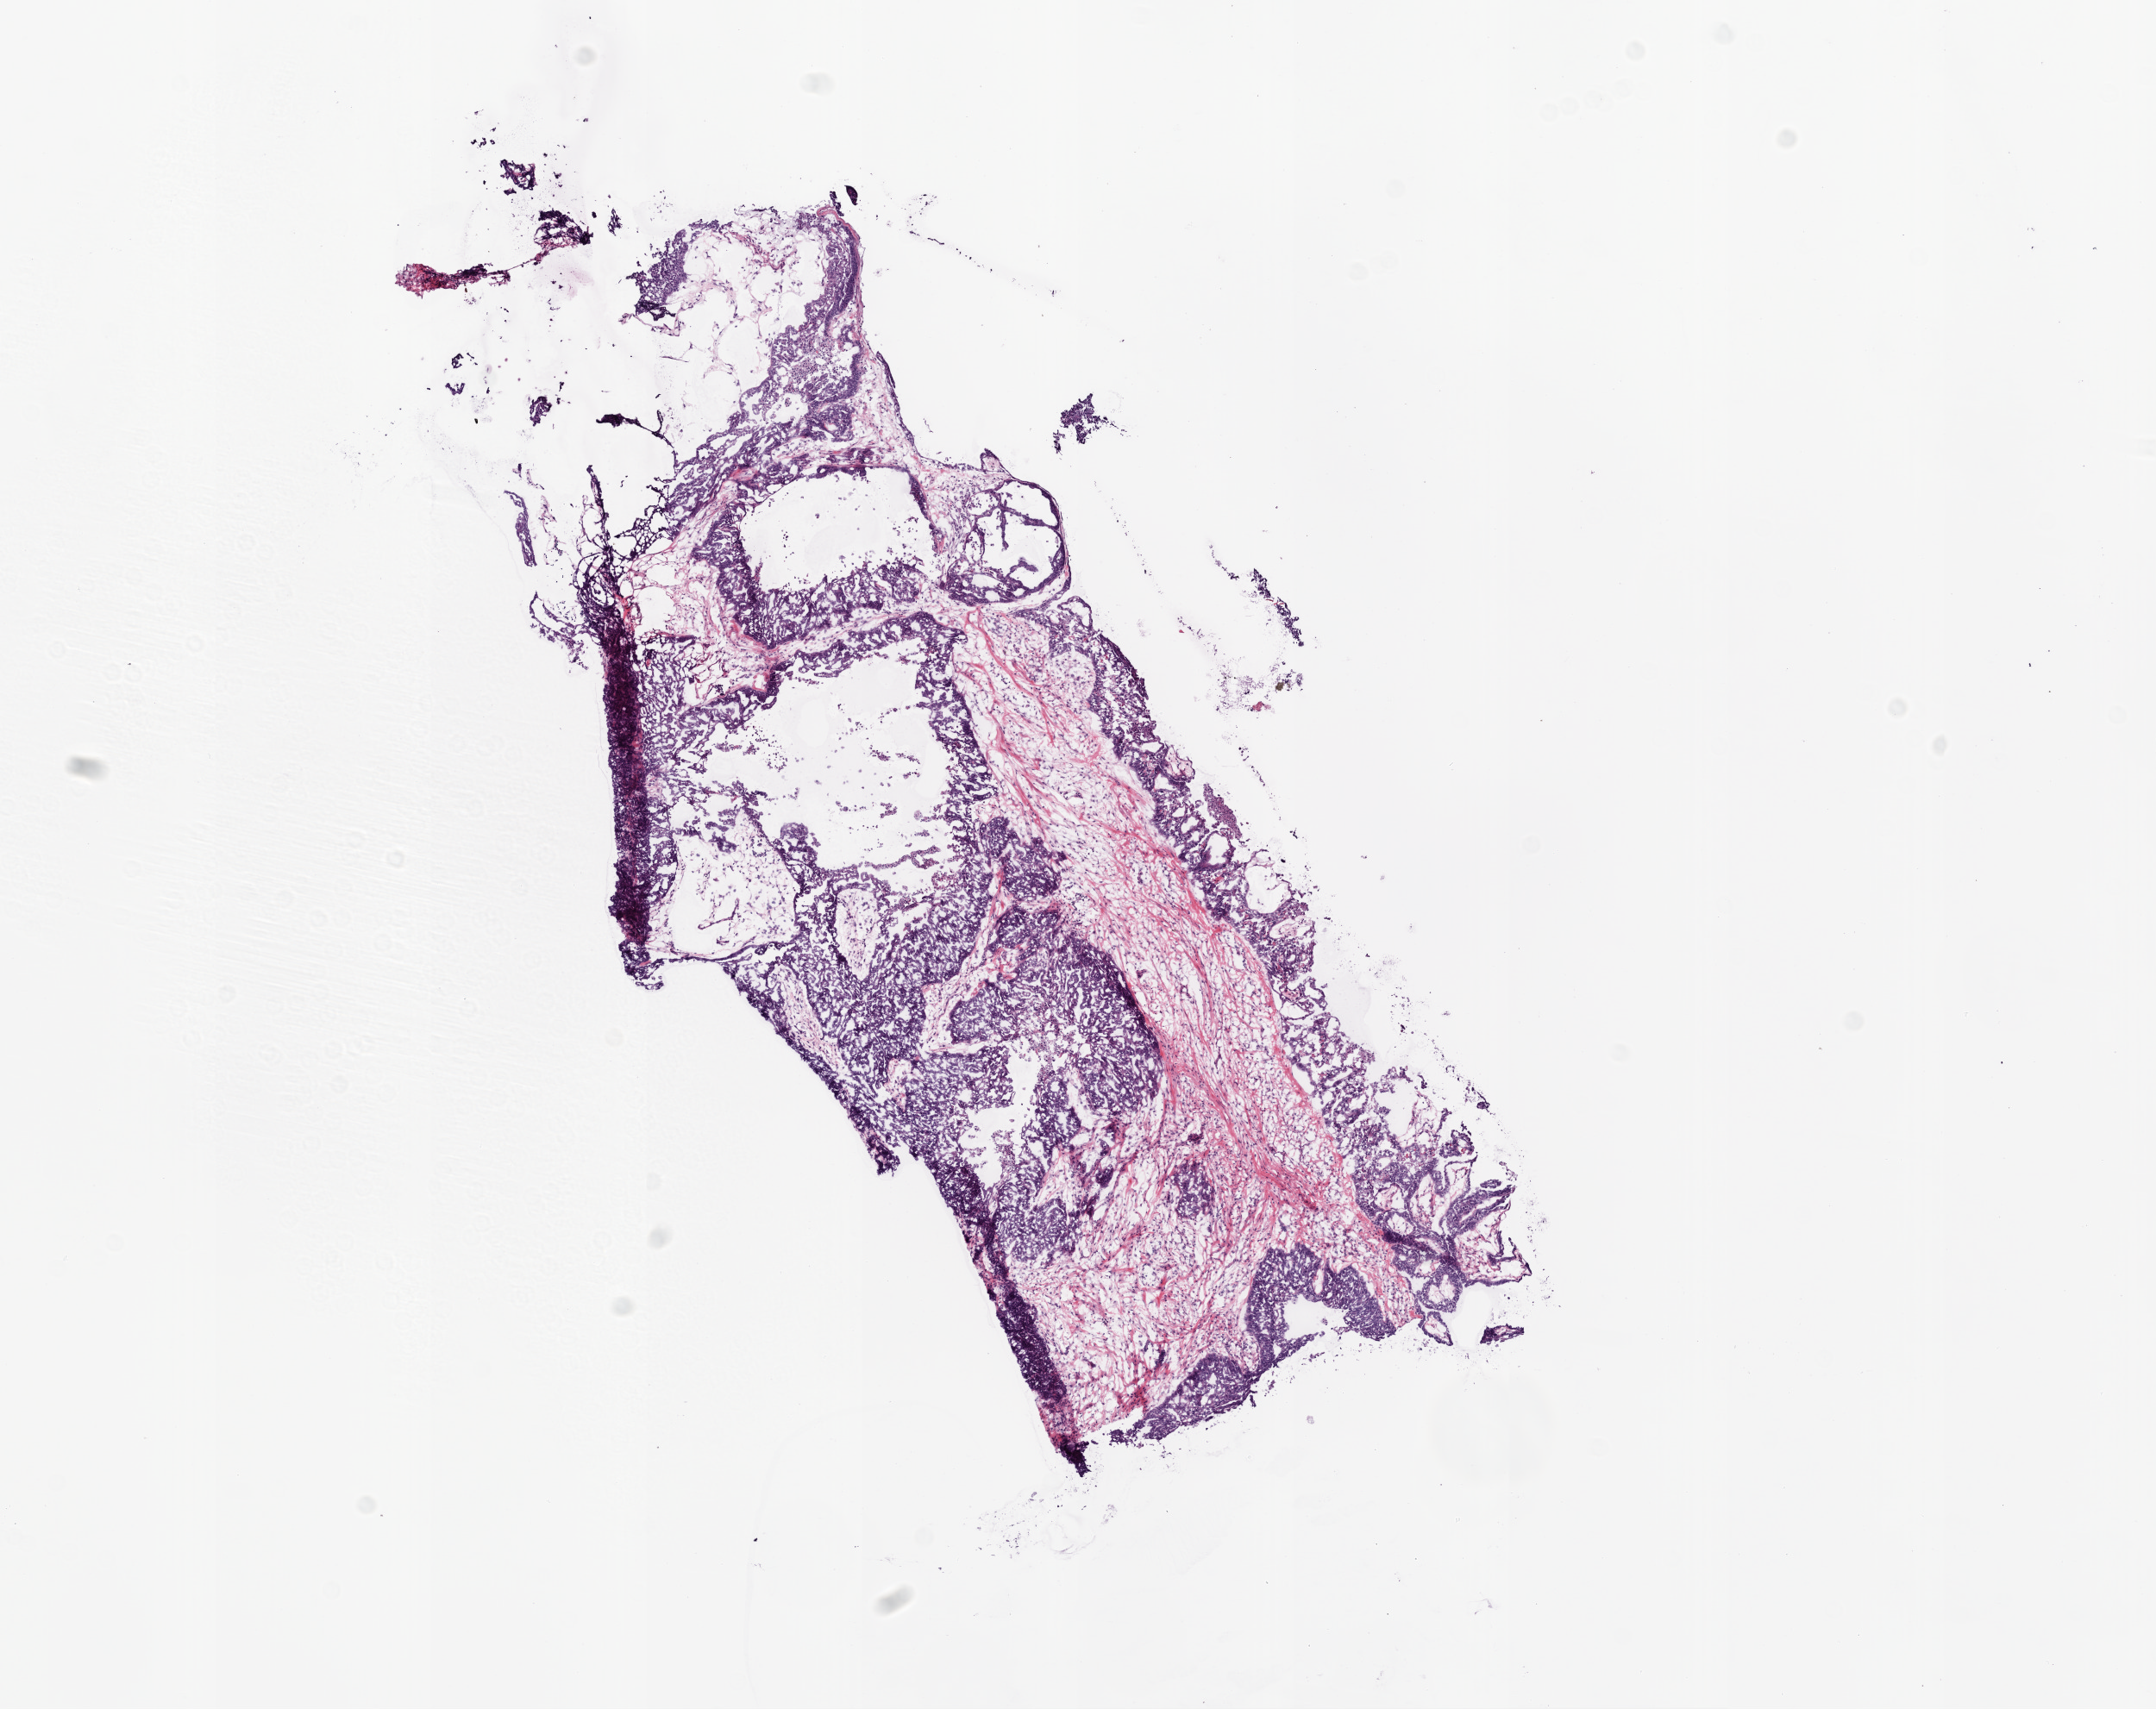
Digitized H&E tissue section (whole slide) — low-resolution overview of the scanned area, about 10.0 x 8.0 mm (from a 20x scan); frozen section from the bottom of the tissue portion; sample: primary tumour, ovary. Female, age 56 years at initial diagnosis. Pathologist review of this section (percent, as recorded): tumour cells 45%, tumour nuclei 70%, normal cells 45%, stromal cells 3%, necrosis 7%.
Diagnosis: Serous cystadenocarcinoma, NOS. FIGO stage: IIIC. Laterality: bilateral.